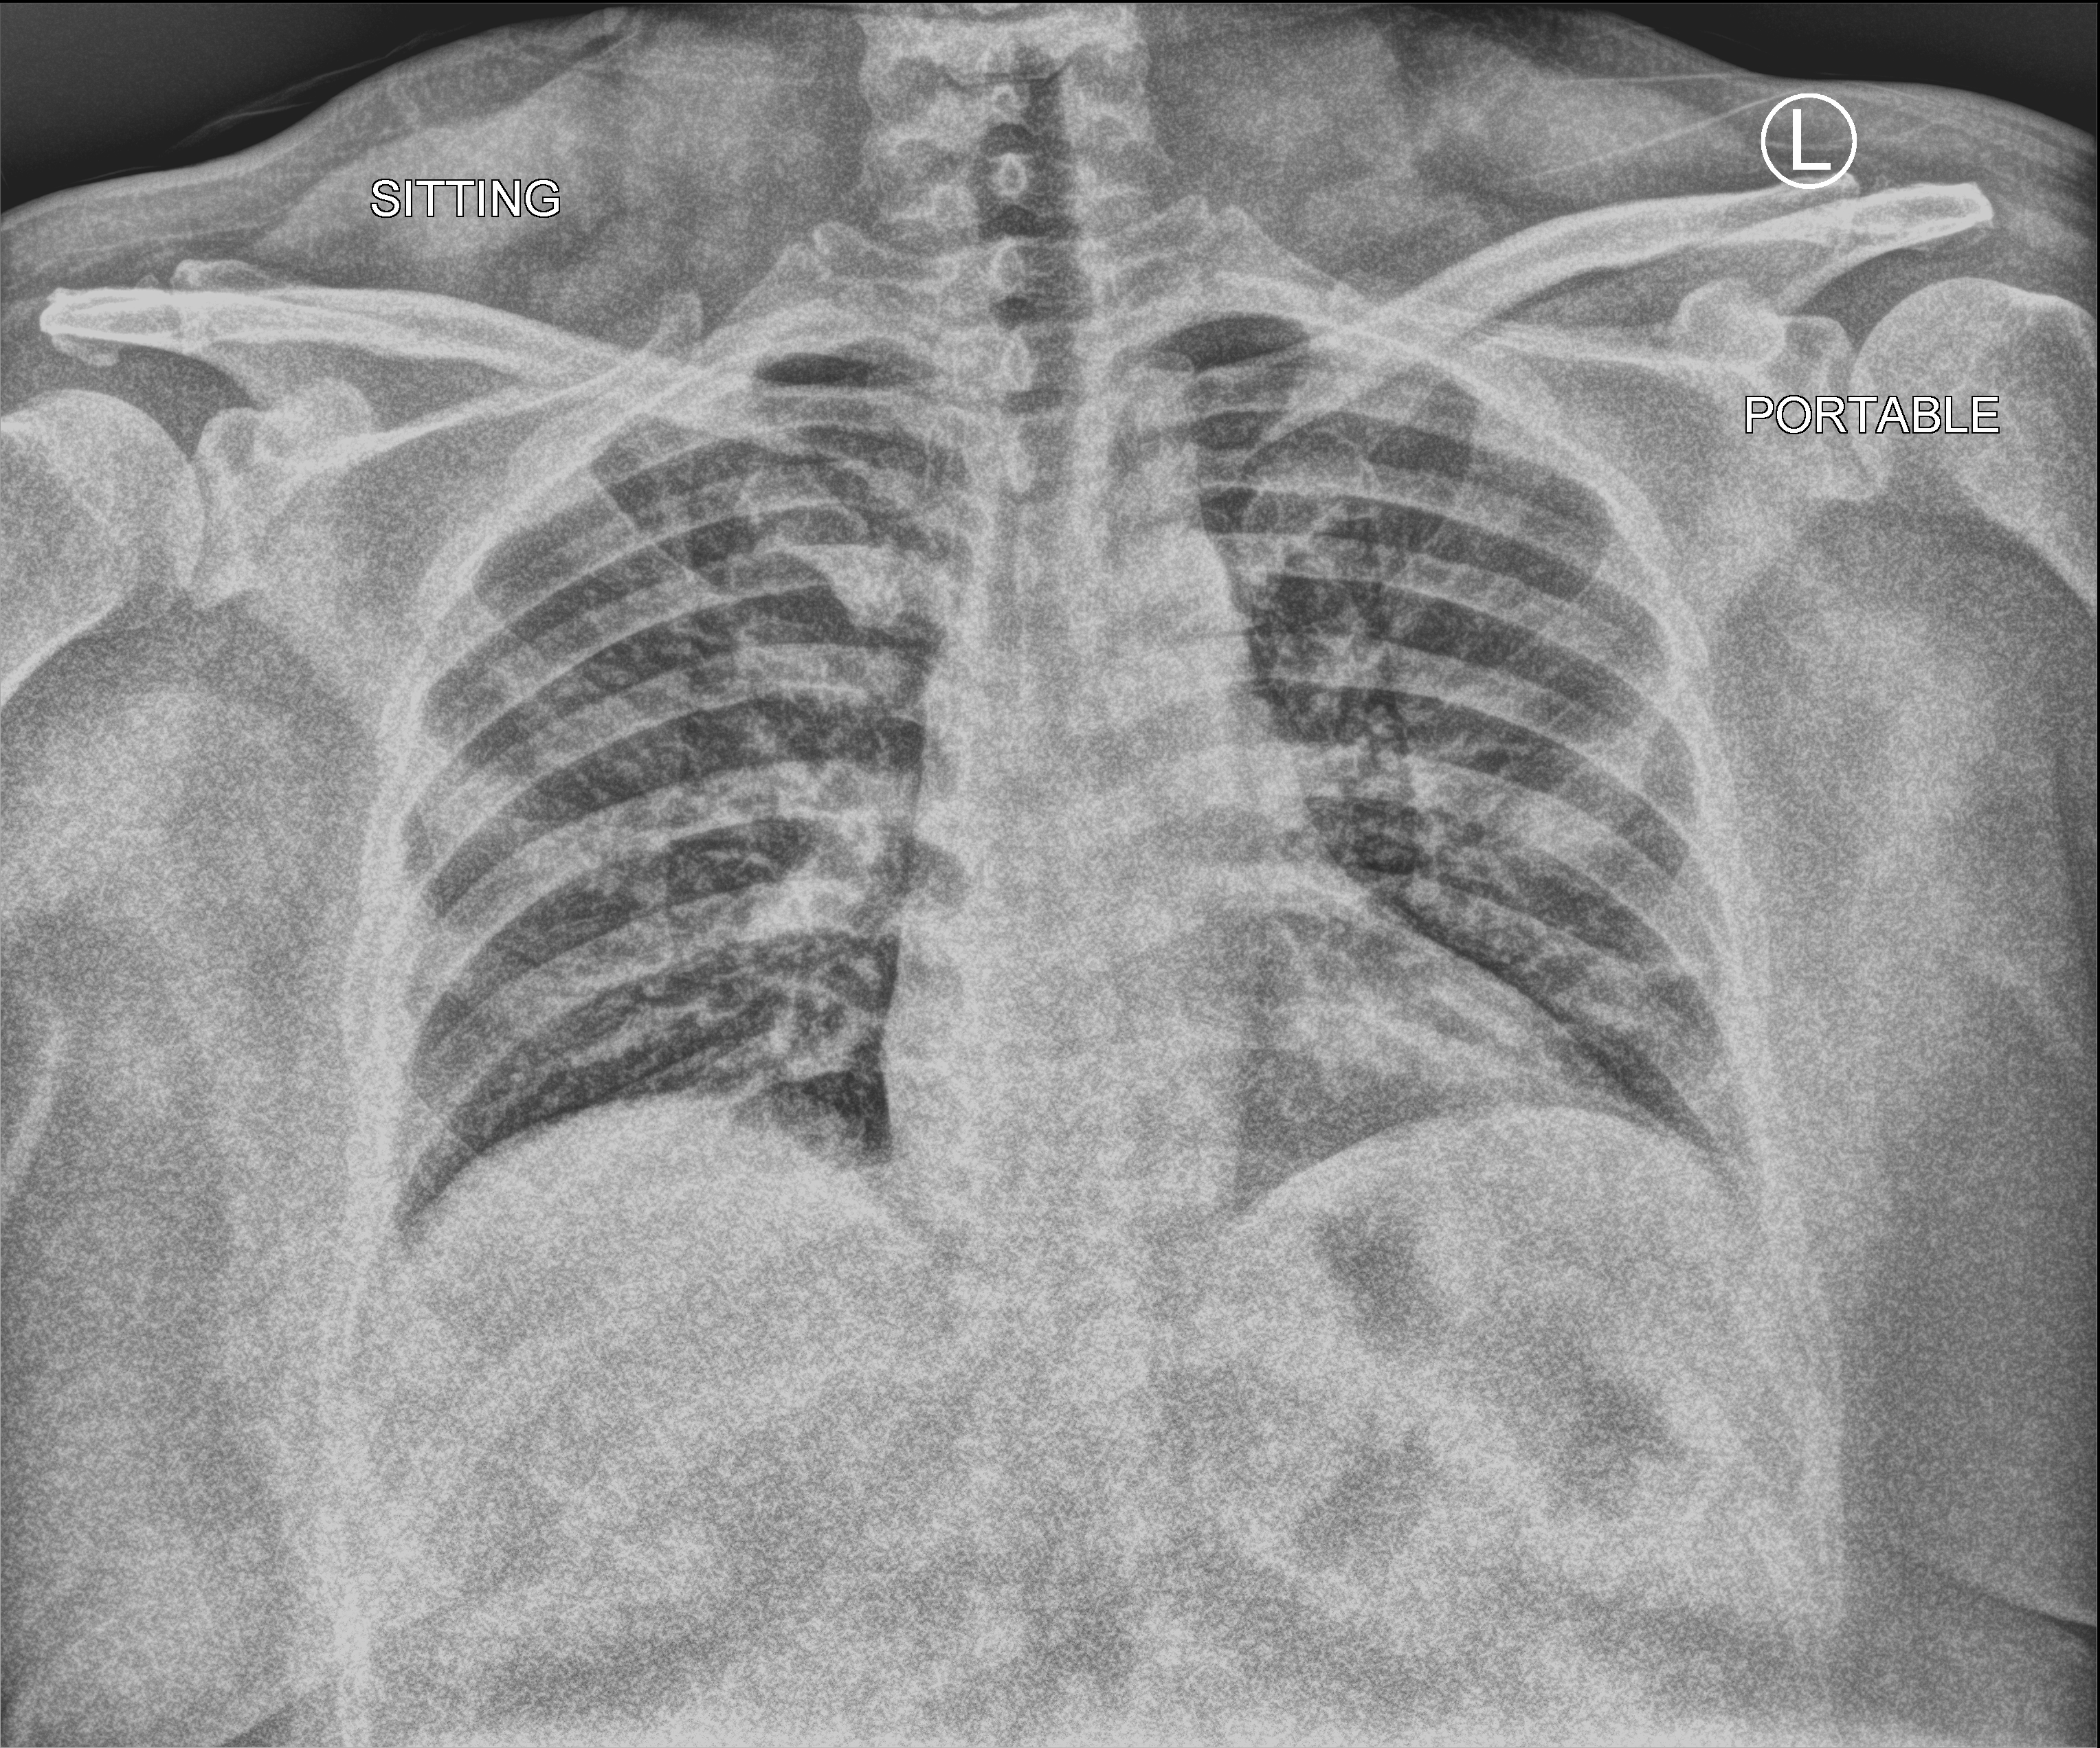
Bedside chest radiograph (computed radiography), anteroposterior (AP) projection. Male patient hospitalised with COVID-19, age 18–59 years.
From the hospital-stay record, not from the radiograph (when in the stay this image was taken is not recorded): admitted to intensive care during this hospital stay: no; length of hospital stay: 1 day; mechanically ventilated during this hospital stay: no.